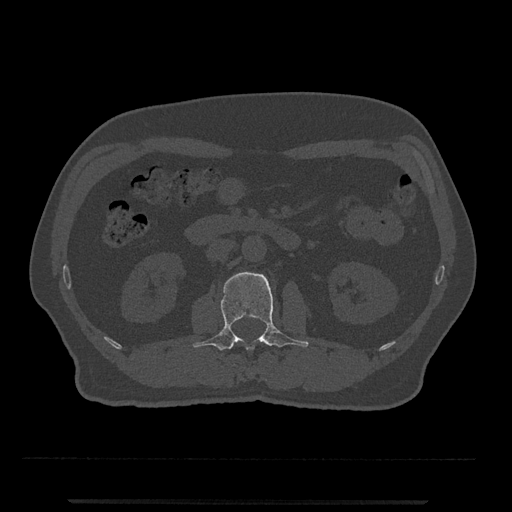
CT including the spine, one axial slice. Slice 274 of 797 in the series (ordered by position). Reconstruction kernel Br40s/3. Bone window (W 1800 / L 400 HU). 512 × 512 image matrix, field of view 419 × 419 mm. Male patient, age 63 years. From the clinical record (not read from this slice): primary cancer: prostate.
Outlined on this slice (semi-automatically segmented with operator editing):
- L2 vertebra: bounding box (x1, y1, x2, y2) in pixels: (193, 272, 309, 351)